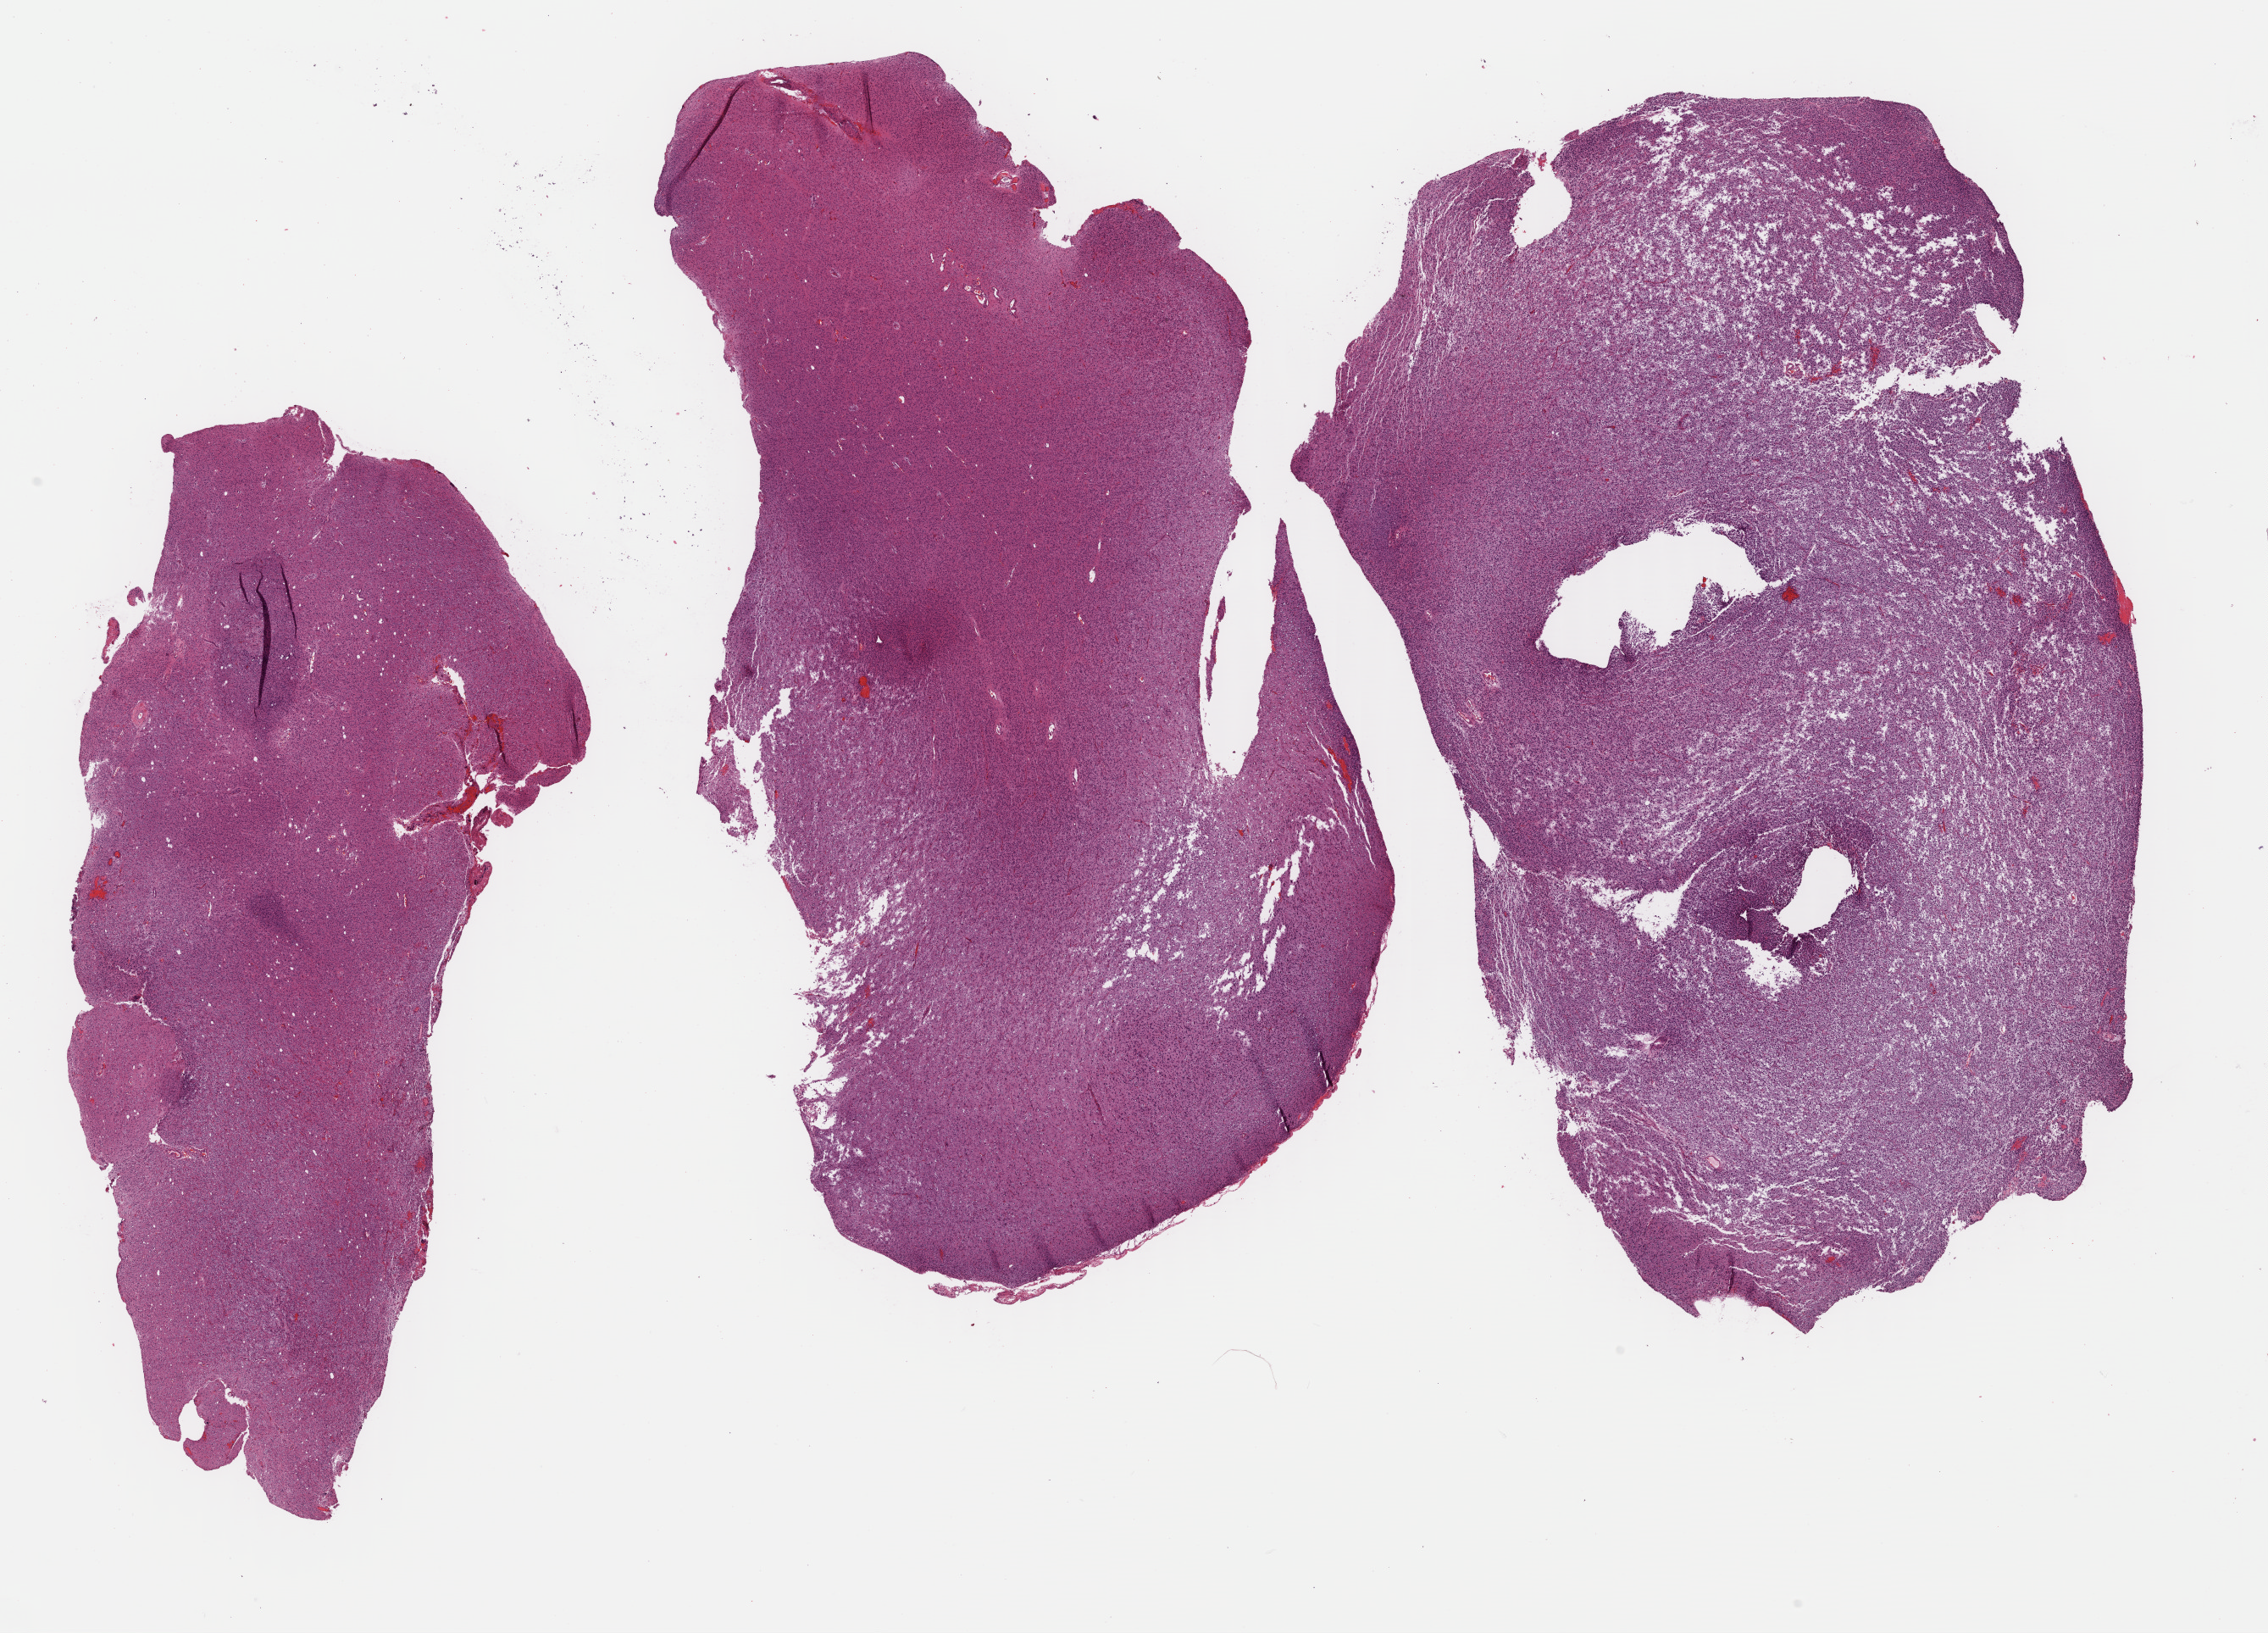
Digitized H&E-stained tissue section (whole slide) — shown as a low-resolution overview of the whole scanned area (about 21.0 x 15.1 mm, slide scanned at 40x); FFPE section; primary tumour sample from the brain. Male, age 30 years at initial diagnosis.
Diagnosis: Oligodendroglioma, anaplastic (cerebrum).